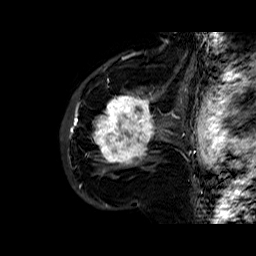
Breast MRI (dynamic contrast-enhanced), one sagittal slice; position 41 of 60 along the scan axis; dynamic contrast-enhanced series, time point 2 of 6 at this slice position (early post-contrast); 1.5 T; TE 6.4 ms, TR 32.8 ms; 4 mm slice thickness; 256 × 256 image matrix, field of view 200 × 200 mm. Female patient. From the clinical record (not read from this slice): setting: breast cancer imaged before/during neoadjuvant chemotherapy; receptor status: HR-positive, HER2-negative.
Outlined on this slice (semi-automatic segmentation, software-assisted and operator-edited):
- analysis volume of interest (the breast-tissue region the enhancement analysis was run in; not a lesion): bounding box <86,77,163,177> (left, top, right, bottom; pixels)
- tumour enhancement mask (voxels above the 100 % enhancement threshold inside the analysis volume of interest): <92,90,157,172>